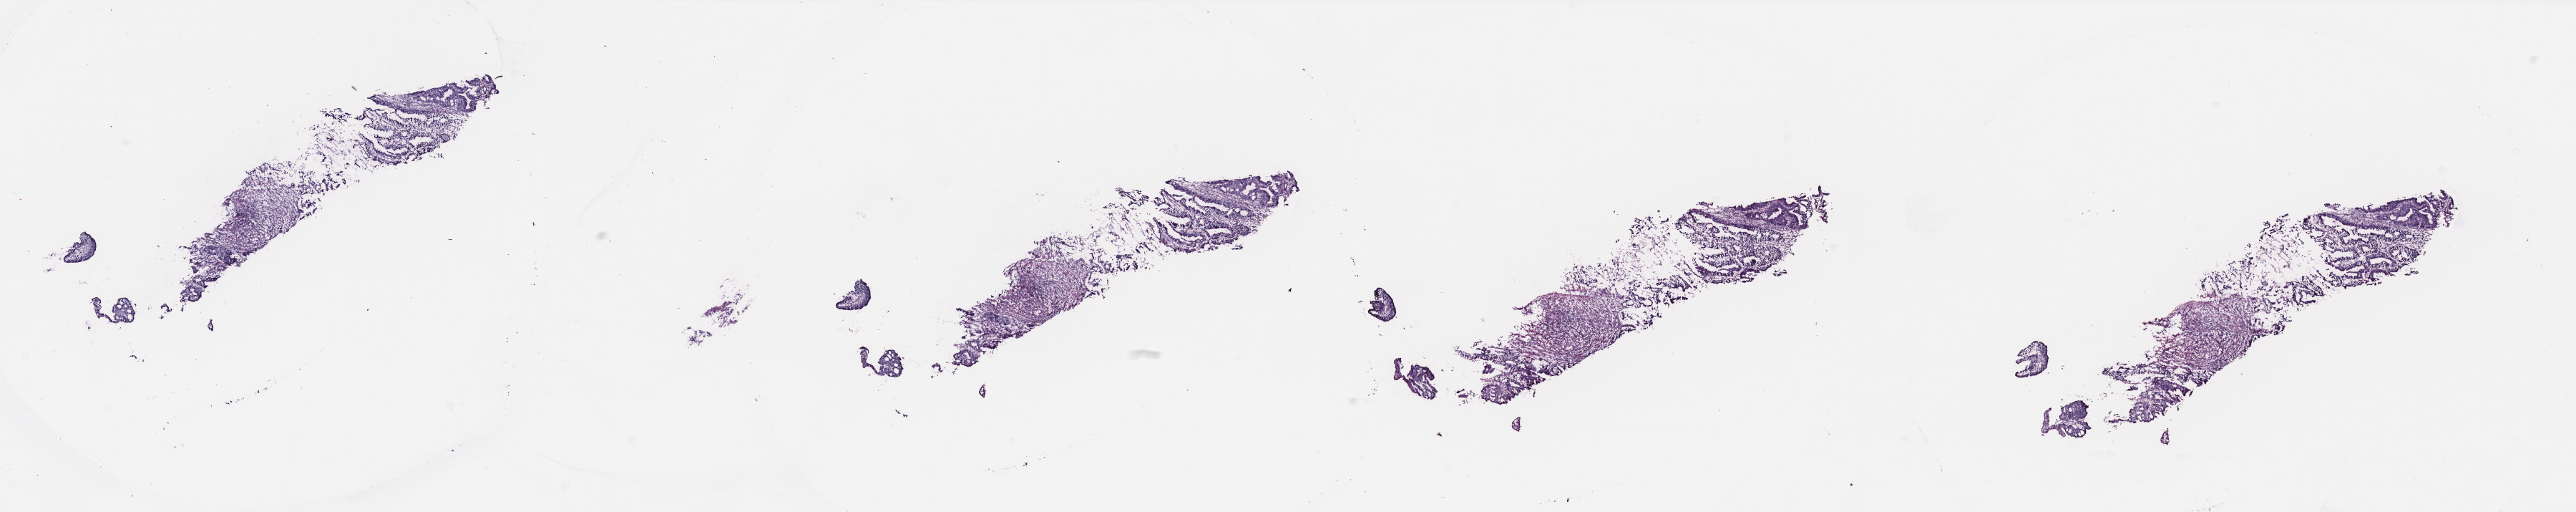
H&E whole-slide image — shown as a low-resolution overview of the whole scanned area (about 28.9 x 5.7 mm, slide scanned at 40x), frozen section, sample: primary tumour, colon. Patient: female, age at initial diagnosis 66 years. Composition of this section per pathologist review: tumour cells 77%, tumour nuclei 65%, normal cells 0%, stromal cells 20%, necrosis 3%. Infiltration values recorded for this section: lymphocyte infiltration 7%, monocyte infiltration 1%, neutrophil infiltration 2%.
AJCC pathologic stage: IIIB (6th edition). Histologic diagnosis: Adenocarcinoma, NOS (sigmoid colon). Lymph nodes positive (case pathology): 1 of 31 examined.